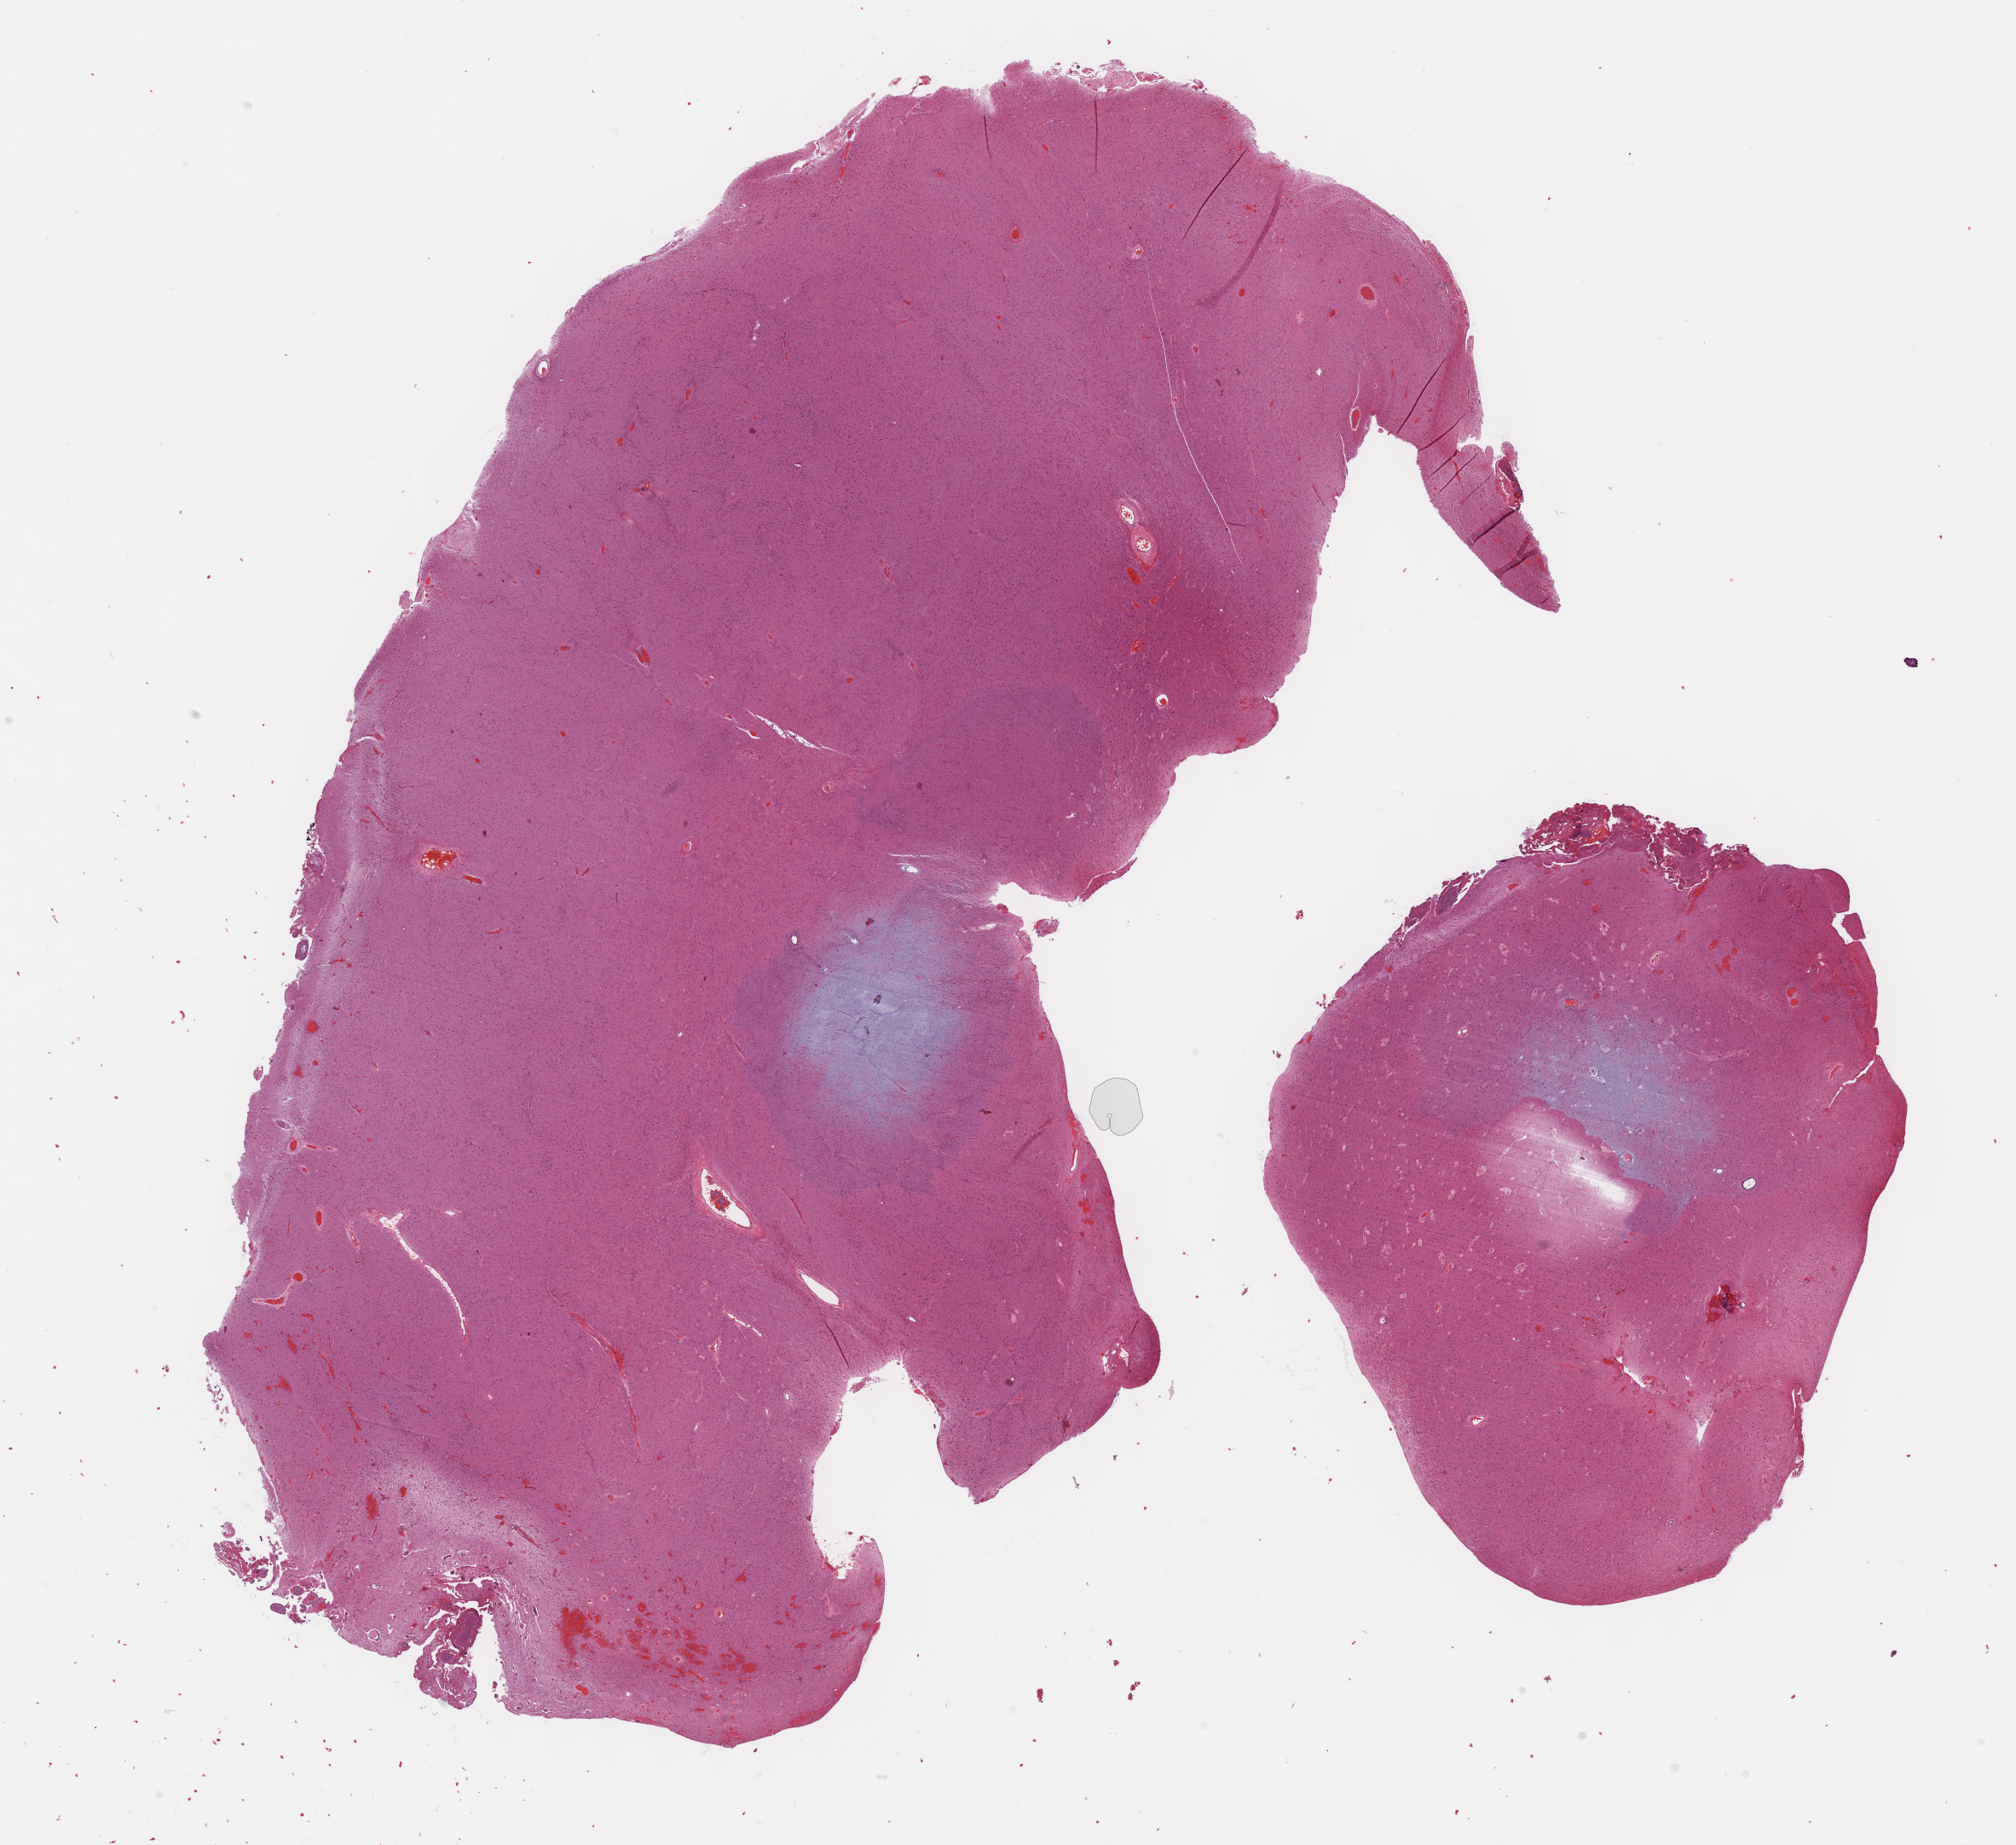
Whole-slide histology image, H&E, shown as a low-resolution overview of the whole scanned area (about 19.1 x 17.5 mm), formalin-fixed paraffin-embedded (FFPE) diagnostic section, sample: primary tumour, brain. Female patient; age at initial diagnosis 32 years. Histologic grade: G2 (moderately differentiated).
• diagnosis: Astrocytoma, NOS
• laterality: midline